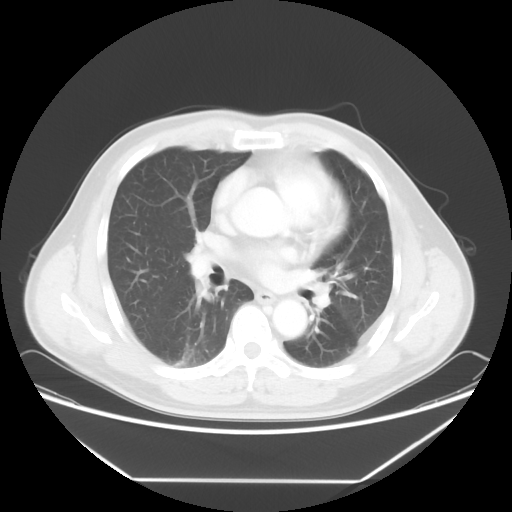
Chest CT, one axial slice. Position 36 of 65 along the scan axis. 120 kVp. Lung window (W 1500 / L -600 HU). 512 × 512 image matrix, field of view 418 × 418 mm. Patient: male, 50 years. Case-level facts recorded for this patient, not image findings: clinical TNM (as recorded): T1c N0 M0; histopathological grade: G3.
Outlined on this slice (rectangle marked by the reading radiologist):
- lung tumour (recorded histology: adenocarcinoma): bounding box <170,342,198,368> (left, top, right, bottom; pixels)